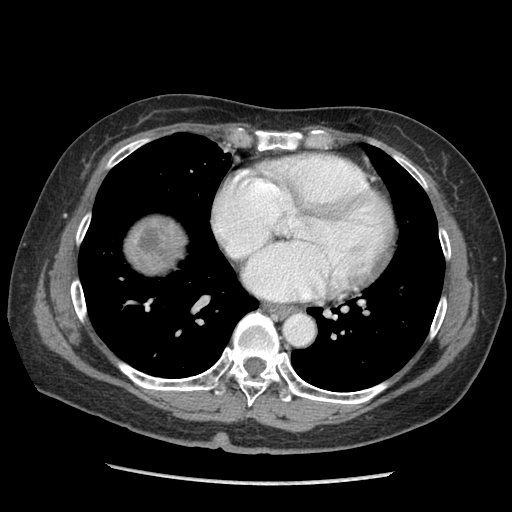
Contrast-enhanced abdominal CT (liver protocol), one axial slice. Position 98 of 105 along the scan axis. Soft-tissue window (W 400 / L 40 HU). 2.5 mm slice thickness. 512 × 512 image matrix. Case-level facts recorded for this patient, not image findings: diagnosis: hepatocellular carcinoma (patient treated with transarterial chemoembolisation; whether this scan precedes or follows treatment is not stated here); TNM stage (as recorded): Stage-I; Child-Pugh class: A.
Structures marked on this image (semi-automatically segmented with operator editing):
- liver parenchyma outside the tumour (the mass and vessels are separate outlines, so this box may not span the whole liver): bounding box [x1, y1, x2, y2] px = [126, 216, 184, 272]
- mass: [137, 227, 165, 262]